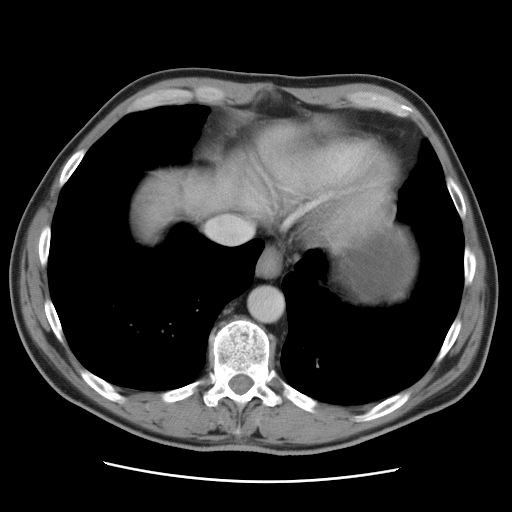
Contrast-enhanced abdominal CT, one axial slice. 120 kVp. Intravenous contrast given. Soft-tissue window (W 400 / L 40 HU). 512 × 512 image matrix, field of view 366 × 366 mm. Male patient, age 59 years. Case-level facts recorded for this patient, not image findings: diagnosis: colorectal cancer liver metastases, imaged before liver resection; multiple liver metastases: yes; largest metastasis: 0.6 cm.
Outlined on this slice (outlined manually by an expert reader):
- liver: bounding box (x1, y1, x2, y2) in pixels: (132, 133, 284, 244)
- planned liver remnant (the part of the liver to remain after resection): (156, 136, 272, 218)